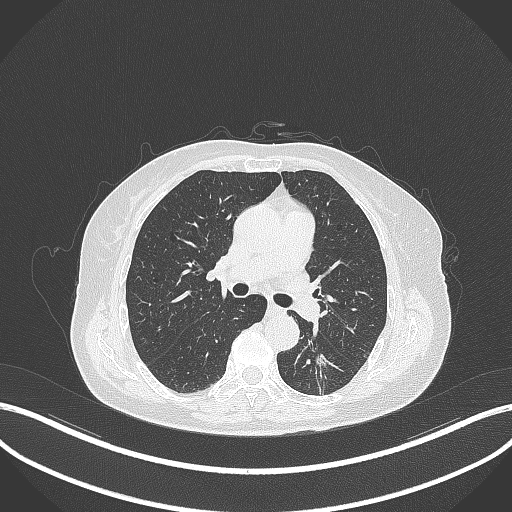
Chest CT, one axial slice; position 174 of 352 along the scan axis; reconstruction kernel B70f; 120 kVp; lung window (W 1500 / L -600 HU); 512 × 512 image matrix, field of view 400 × 400 mm. Patient: female, 70 years. Case-level facts recorded for this patient, not image findings: clinical TNM (as recorded): T1c N0 M0.
Structures marked on this image (rectangle marked by the reading radiologist):
- lung tumour (recorded histology: adenocarcinoma): bounding box <311,345,331,376> (left, top, right, bottom; pixels)